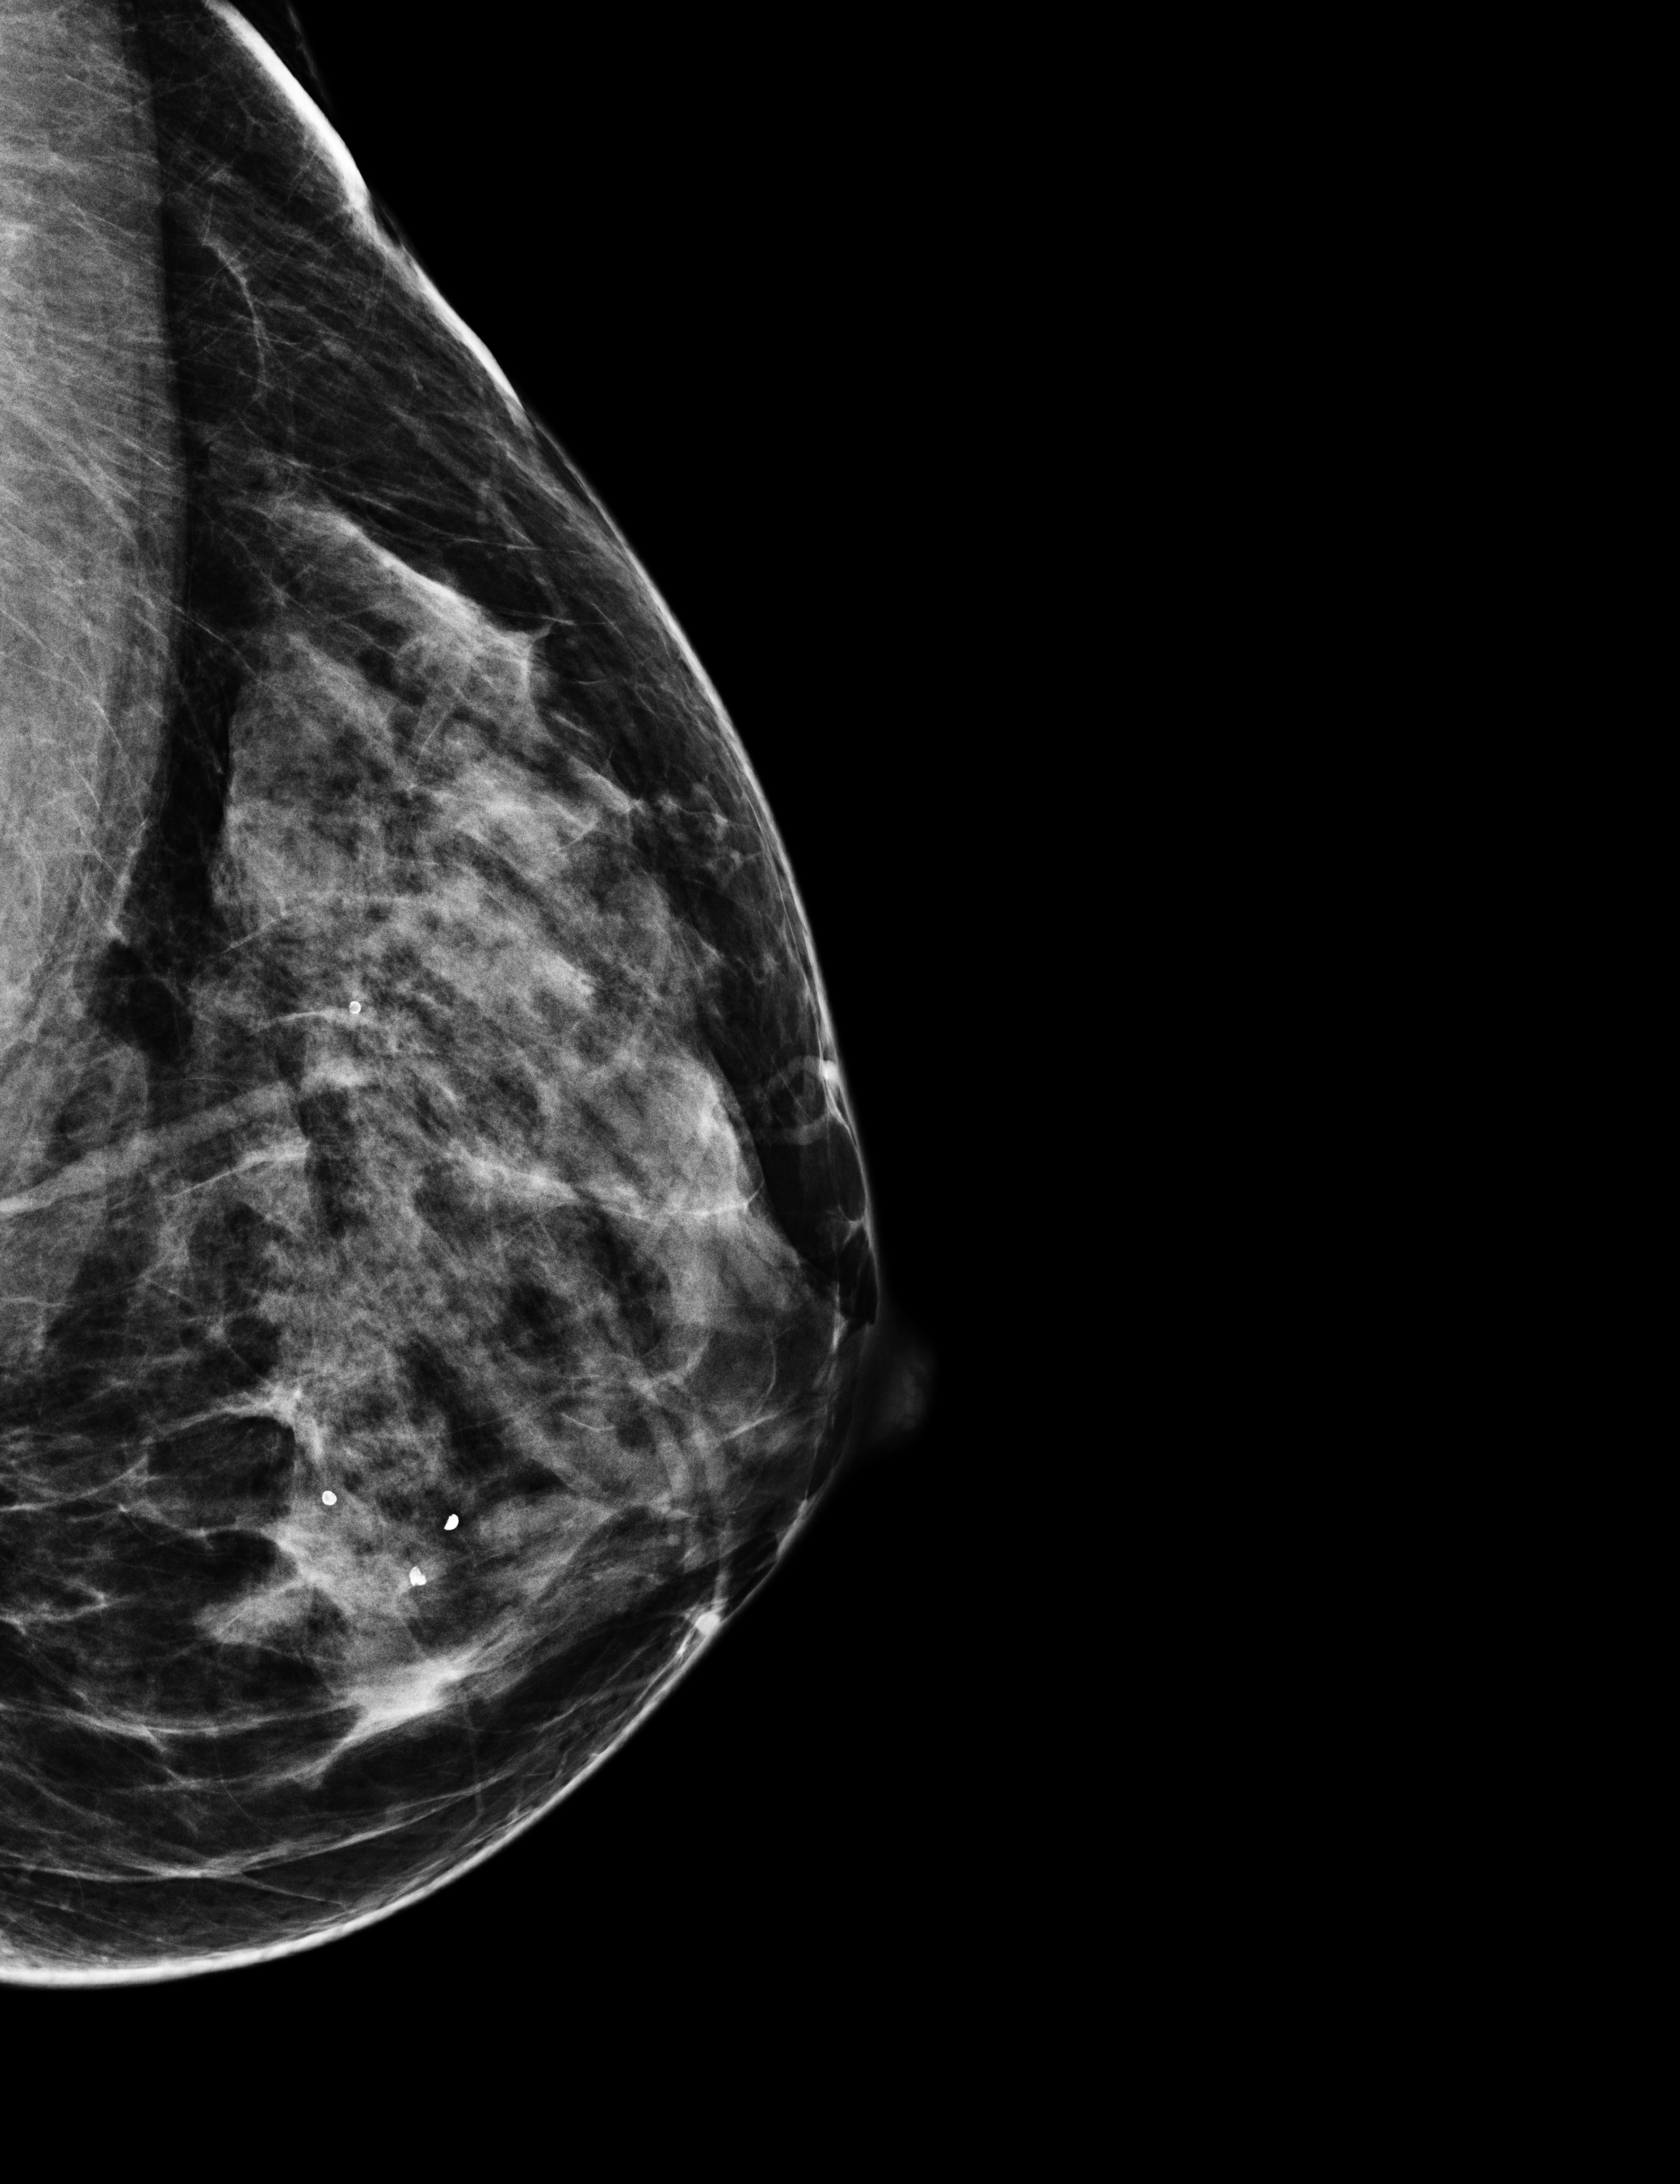
Full-field digital mammogram (FFDM), left breast, laterally exaggerated craniocaudal (XCCL) view, annual screening mammography examination, system: Selenia Dimensions. Patient: female, 47 years.
Breast density at the screening exam (both breasts): heterogeneously dense (BI-RADS density category c). Final BI-RADS category for the screening round (tomosynthesis exam, both breasts): category 2. Recall: no recall after this screen.